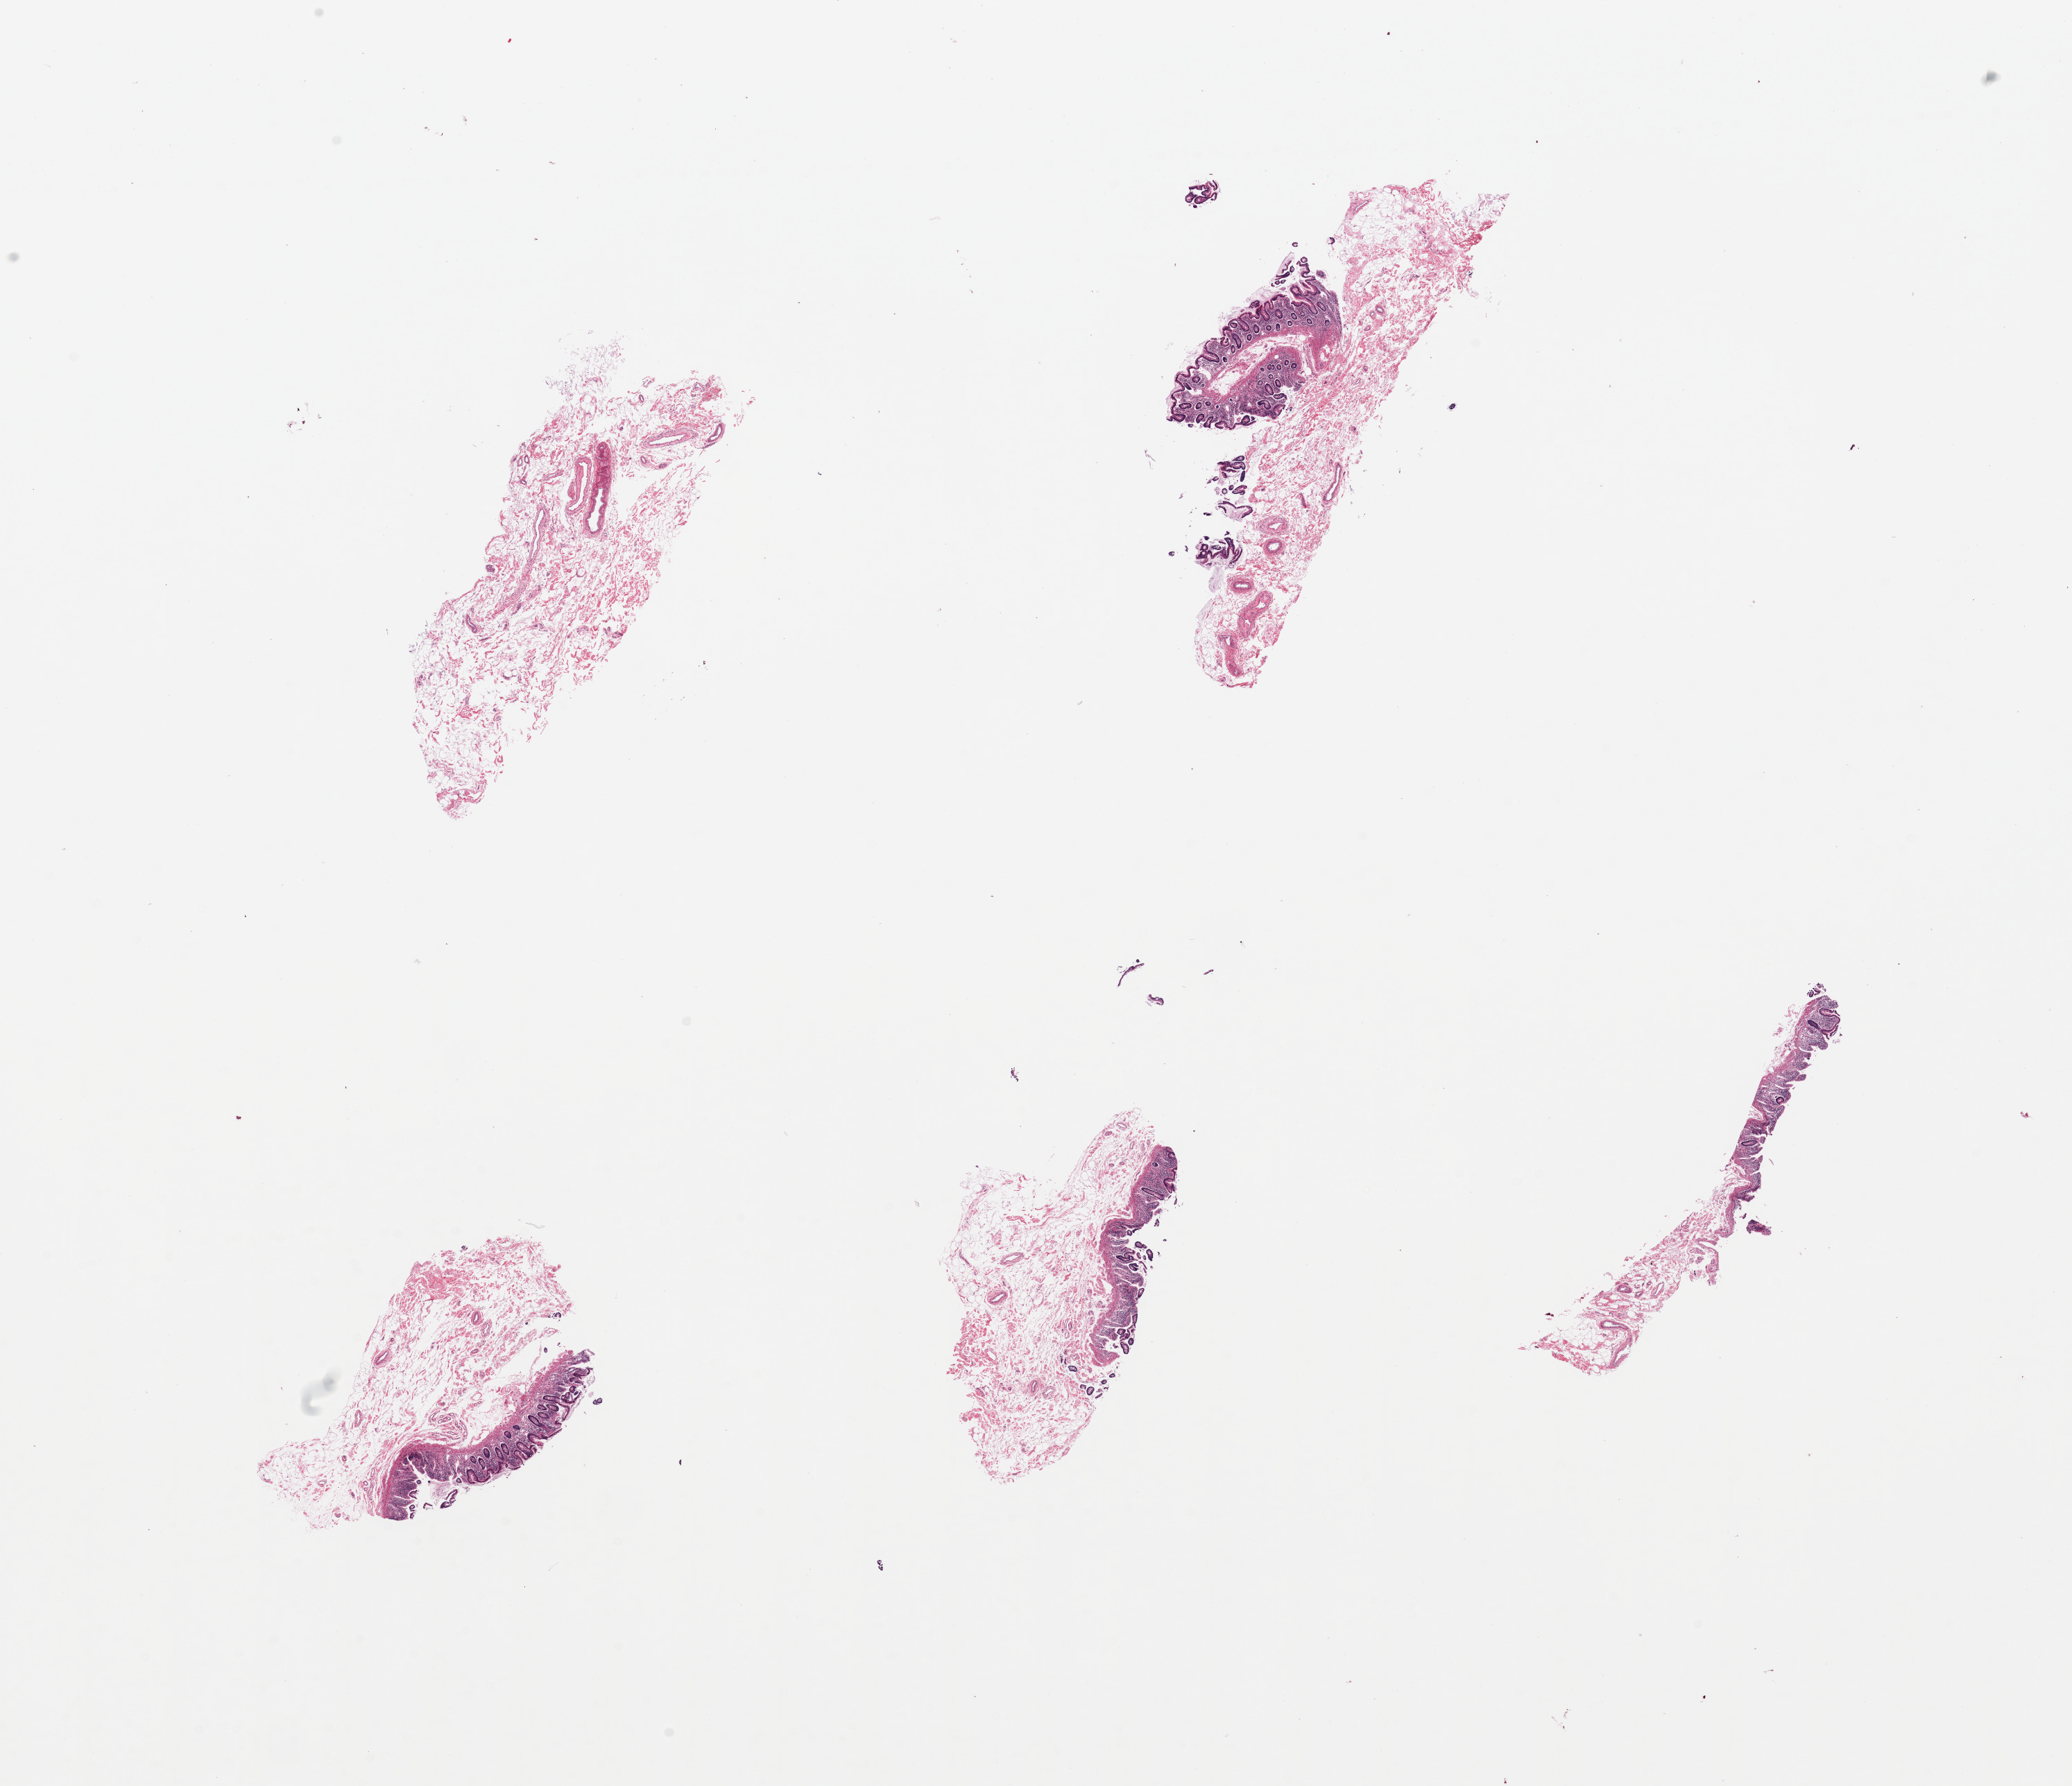
Whole-slide image, H&E stain, low-resolution overview of the scanned area, about 23.6 x 20.4 mm; PAXgene-fixed, paraffin-embedded tissue; sampled site (target tissue): ileum; donor tissue sample. Donor sex: female.
- pathologist's review note for this sample: 5 pieces, predominantly submucosa and strips of colonic mucosa